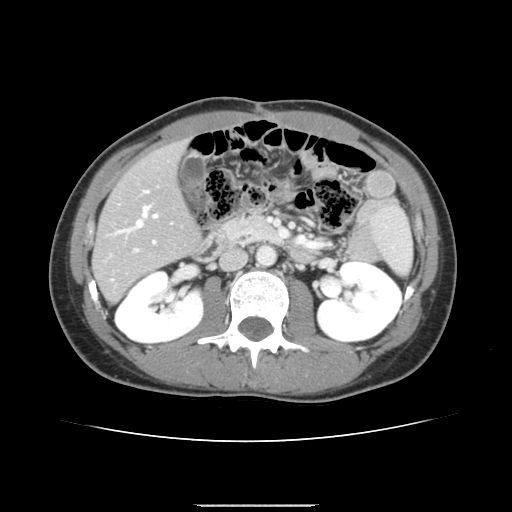
Contrast-enhanced abdominal CT, one axial slice. 120 kVp. Intravenous contrast given. Soft-tissue window (W 400 / L 40 HU). 2.5 mm slice thickness. 512 × 512 image matrix. Female patient, age 32 years. Case-level facts recorded for this patient, not image findings: diagnosis: colorectal cancer liver metastases, imaged before liver resection; multiple liver metastases: yes; largest metastasis: 0.7 cm.
Annotated regions visible in this slice (outlined manually by an expert reader):
- hepatic veins: box from (x=125, y=206) to (x=157, y=231) px
- liver: (x=94, y=144)–(x=199, y=300)
- planned liver remnant (the part of the liver to remain after resection): (x=94, y=144)–(x=199, y=293)
- portal vein (with intrahepatic branches): (x=111, y=190)–(x=156, y=280)